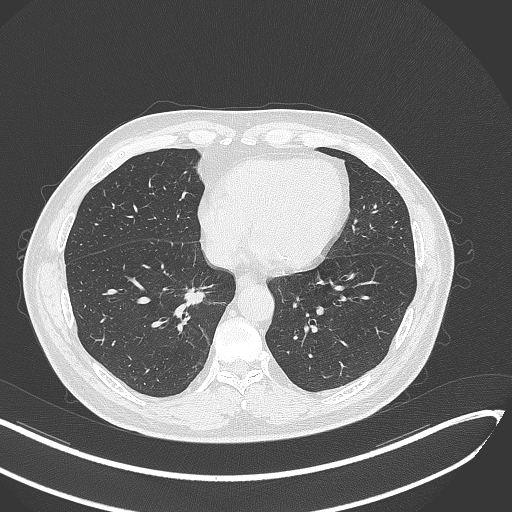
Chest CT, one axial slice. Position 132 of 429 along the scan axis. 120 kVp. Lung window (W 1500 / L -600 HU). 1 mm slice thickness. 512 × 512 image matrix. Patient: male, 62 years. Case-level facts recorded for this patient, not image findings: clinical TNM (as recorded): T1b N0 M0; histopathological grade: G2.
Annotated regions visible in this slice (bounding box drawn by a radiologist):
- lung tumour (recorded histology: adenocarcinoma): bounding box [x1, y1, x2, y2] px = [180, 287, 216, 310]